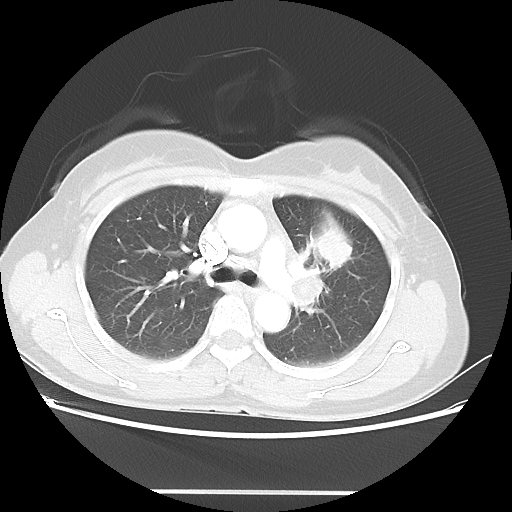
Chest CT, one axial slice; position 30 of 46 along the scan axis; reconstruction kernel LUNG; lung window (W 1500 / L -600 HU); 512 × 512 image matrix, field of view 360 × 360 mm. Patient: female, 50 years. Case-level facts recorded for this patient, not image findings: clinical TNM (as recorded): T1c N1 M0; histopathological grade: G3.
Structures marked on this image (bounding box drawn by a radiologist):
- lung tumour (recorded histology: adenocarcinoma): bounding box <309,220,355,266> (left, top, right, bottom; pixels)